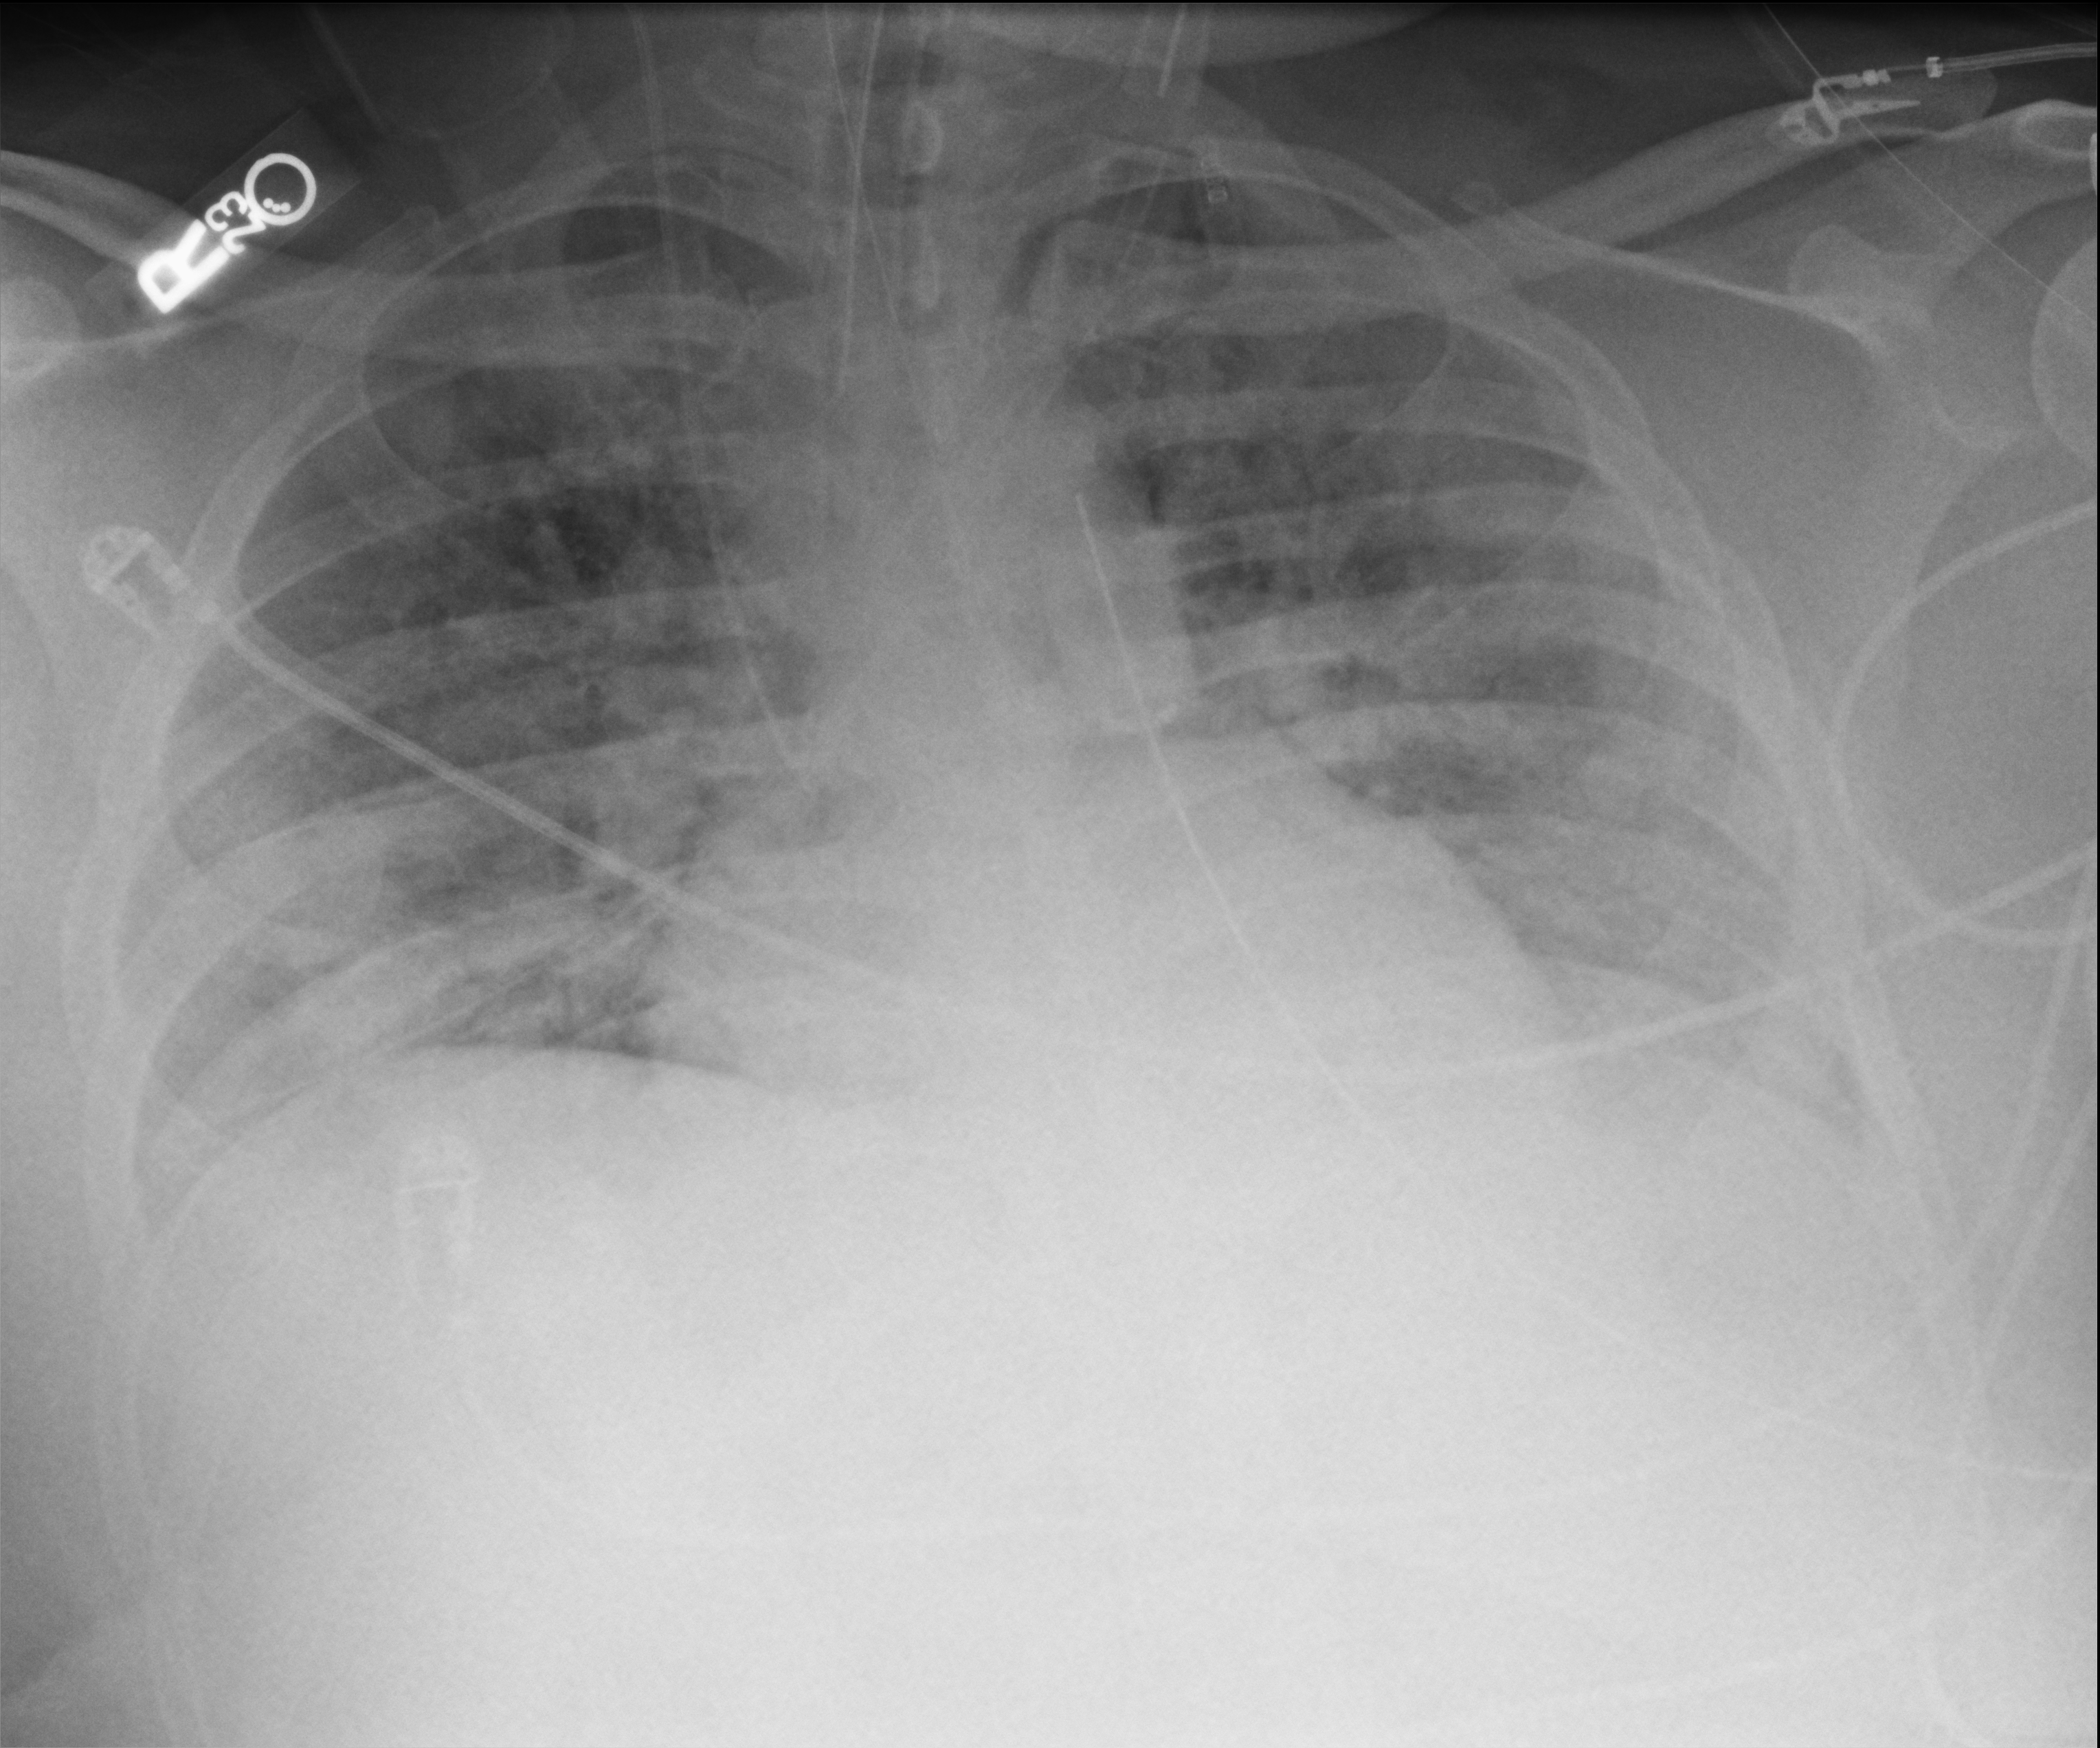
Chest X-ray (portable); anteroposterior (AP) projection. Patient hospitalised with COVID-19; male, aged 18–59 years.
Hospital-stay facts (about this admission, not read from this image; timing relative to this image not recorded): diabetes (admission record): yes.